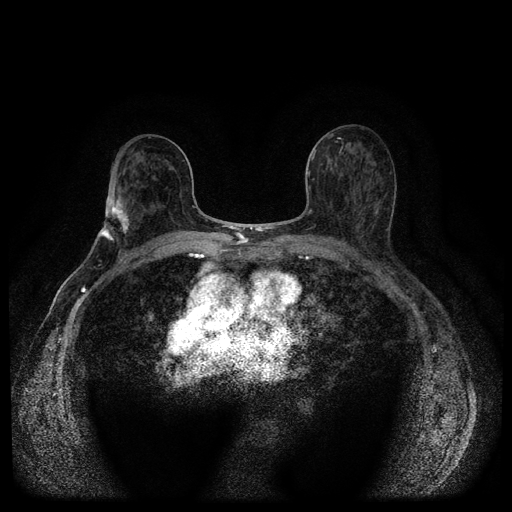
Breast MRI (dynamic contrast-enhanced, multi-phase), one axial slice; slice 58 of 116 in the series (ordered by position); dynamic contrast-enhanced series, time point 2 of 5 at this slice position (early post-contrast); 1.5 T; TE 2.7 ms, TR 5.4 ms; 512 × 512 image matrix, field of view 340 × 340 mm. Female patient, age 75 years.
Outlined on this slice (semi-automatically segmented with operator editing):
- breast lesion (labelled 'tumour' in the annotation; benign lesions carry a separate 'benign' label): bounding box (x1, y1, x2, y2) in pixels: (98, 197, 131, 244)